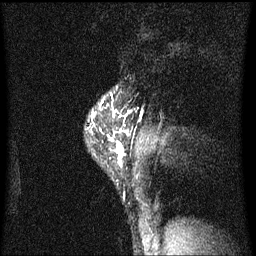
Breast MRI (dynamic contrast-enhanced), one sagittal slice. Position 50 of 60 along the scan axis. Dynamic contrast-enhanced series, image 2 of 3 at this slice position (ordered by acquisition). 1.5 T. TE 4.2 ms, TR 8.4 ms. 2 mm slice thickness. 256 × 256 image matrix, field of view 200 × 200 mm. Patient: female, 40 years.
Annotated regions visible in this slice (semi-automatically segmented with operator editing):
- analysis volume of interest (the breast-tissue region the enhancement analysis was run in; not a lesion): box from (x=90, y=94) to (x=127, y=165) px
- tumour enhancement mask (voxels above the 70 % enhancement threshold inside the analysis volume of interest): (x=93, y=94)–(x=127, y=165)